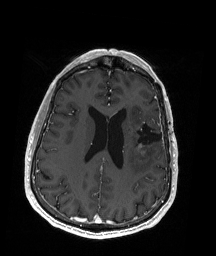
Brain MRI from a brain-tumour surgery series, one axial slice; slice 75 of 192 in the series (ordered by position); T1-weighted post-contrast; 216 × 256 image matrix. Case-level facts recorded for this patient, not image findings: histopathology: Oligodendroglioma; WHO grade: 2; IDH mutation: yes.
Outlined on this slice (outlined manually by an expert reader):
- previous resection cavity: bounding box (x1, y1, x2, y2) in pixels: (132, 121, 163, 148)
- tumour: (137, 120, 153, 155)